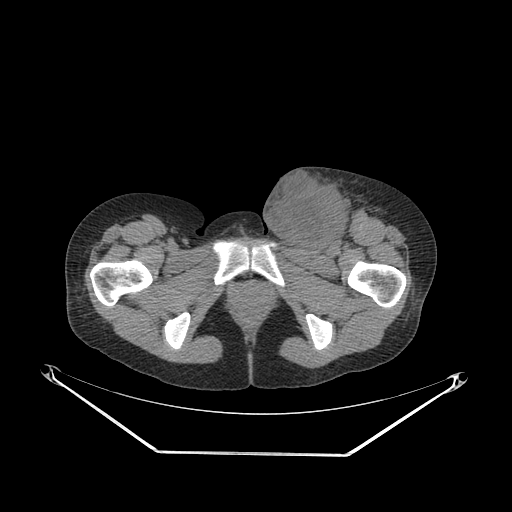
CT of an extremity soft-tissue mass (from a PET/CT study), one axial slice; slice 60 of 267 in the series (ordered by position); 140 kVp; soft-tissue window (W 400 / L 40 HU); 3.75 mm slice thickness; 512 × 512 image matrix, field of view 500 × 500 mm. Female patient. Case-level facts recorded for this patient, not image findings: histological type: leiomyosarcoma; grade: high; site of the primary tumour: groin.
Annotated regions visible in this slice (expert contour drawn on MRI and transferred to this co-registered scan by the dataset authors):
- gross tumour volume including surrounding oedema: box from (x=258, y=169) to (x=373, y=254) px
- gross tumour volume (mass): (x=260, y=174)–(x=348, y=250)